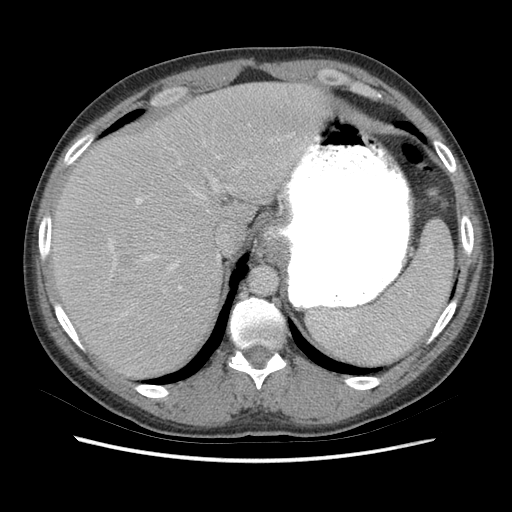
Contrast-enhanced abdominal CT (liver protocol), one axial slice. Slice 53 of 73 in the series (ordered by position). Reconstruction kernel STANDARD. 140 kVp. Soft-tissue window (W 400 / L 40 HU). 2.5 mm slice thickness. 512 × 512 image matrix, field of view 360 × 360 mm. From the clinical record (not read from this slice): diagnosis: hepatocellular carcinoma (patient treated with transarterial chemoembolisation; whether this scan precedes or follows treatment is not stated here); TNM stage (as recorded): Stage-IIIA; Child-Pugh class: A; tumour nodularity: multinodular; tumour size: 6.6 cm.
Structures marked on this image (semi-automatically segmented with operator editing):
- liver parenchyma outside the tumour (the mass and vessels are separate outlines, so this box may not span the whole liver): bounding box [x1, y1, x2, y2] px = [50, 82, 332, 378]
- liver vessels: [108, 136, 319, 316]